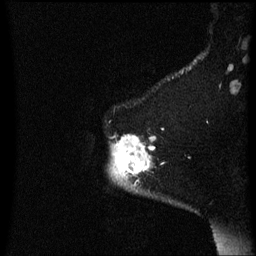
Breast MRI (dynamic contrast-enhanced), one sagittal slice; position 53 of 60 along the scan axis; dynamic contrast-enhanced series, image 2 of 3 at this slice position (ordered by acquisition); 1.5 T; TE 4.2 ms, TR 8.4 ms; 2 mm slice thickness; 256 × 256 image matrix, field of view 200 × 200 mm. Female patient, age 54 years. From the clinical record (not read from this slice): setting: breast cancer imaged before/during neoadjuvant chemotherapy; receptor status: HR-positive, HER2-negative.
Structures marked on this image (semi-automatically segmented with operator editing):
- analysis volume of interest (the breast-tissue region the enhancement analysis was run in; not a lesion): box from (x=110, y=136) to (x=157, y=191) px
- tumour enhancement mask (voxels above the 70 % enhancement threshold inside the analysis volume of interest): (x=112, y=136)–(x=157, y=181)